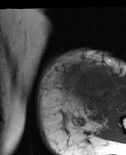
MRI of an extremity soft-tissue mass, one axial slice; slice 20 of 86 in the series (ordered by position); MR volume resampled by the dataset authors to the PET/CT grid (not the native acquisition matrix); 126 × 155 image matrix, field of view 123 × 151 mm. Female patient. From the clinical record (not read from this slice): histological type: pleiomorphic leiomyosarcoma; grade: high; site of the primary tumour: left biceps.
Annotated regions visible in this slice (expert contour drawn on MRI and transferred to this co-registered scan by the dataset authors):
- gross tumour volume including surrounding oedema: bounding box <59,63,119,112> (left, top, right, bottom; pixels)
- gross tumour volume (mass): <59,63,115,100>